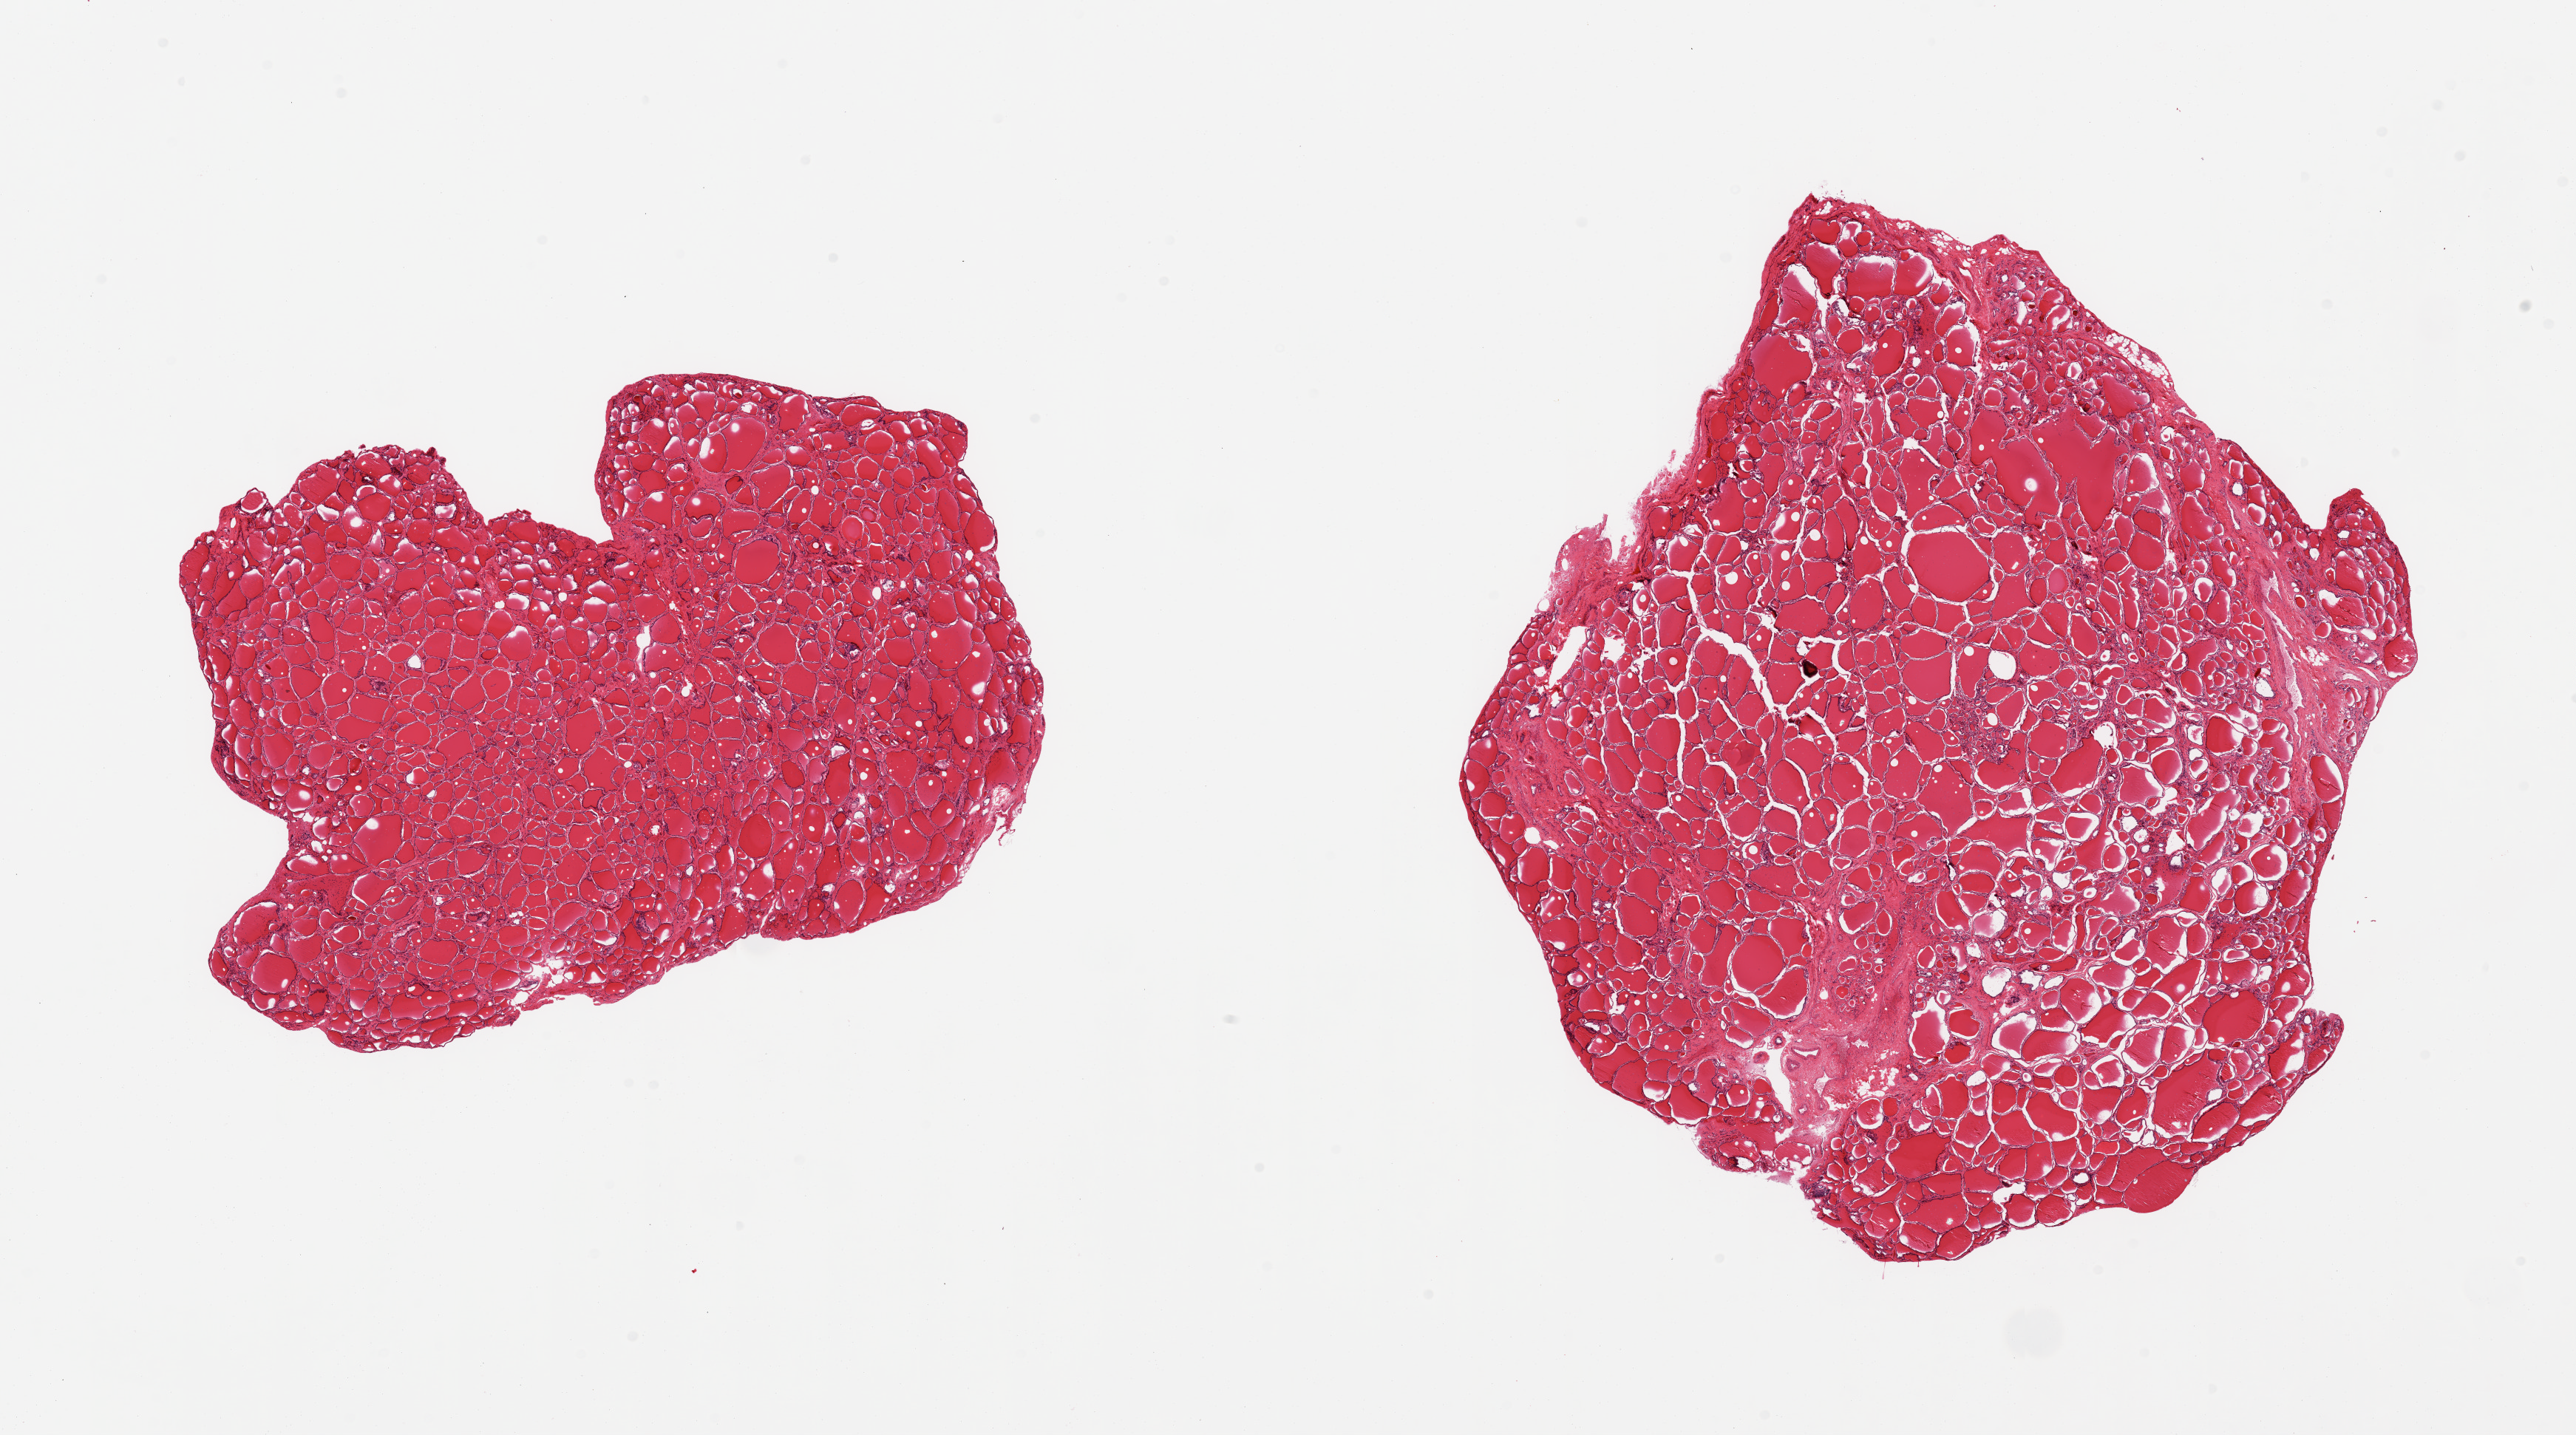
H&E whole-slide image, brightfield, a low-resolution overview of the entire scanned area, about 27.6 x 15.4 mm (acquisition: 20x scan). PAXgene-fixed paraffin-embedded (PFPE) section. Sampled site (target tissue): thyroid. Donor tissue sample. Donor: male.
Pathologist's review note for this sample: 2 pieces.